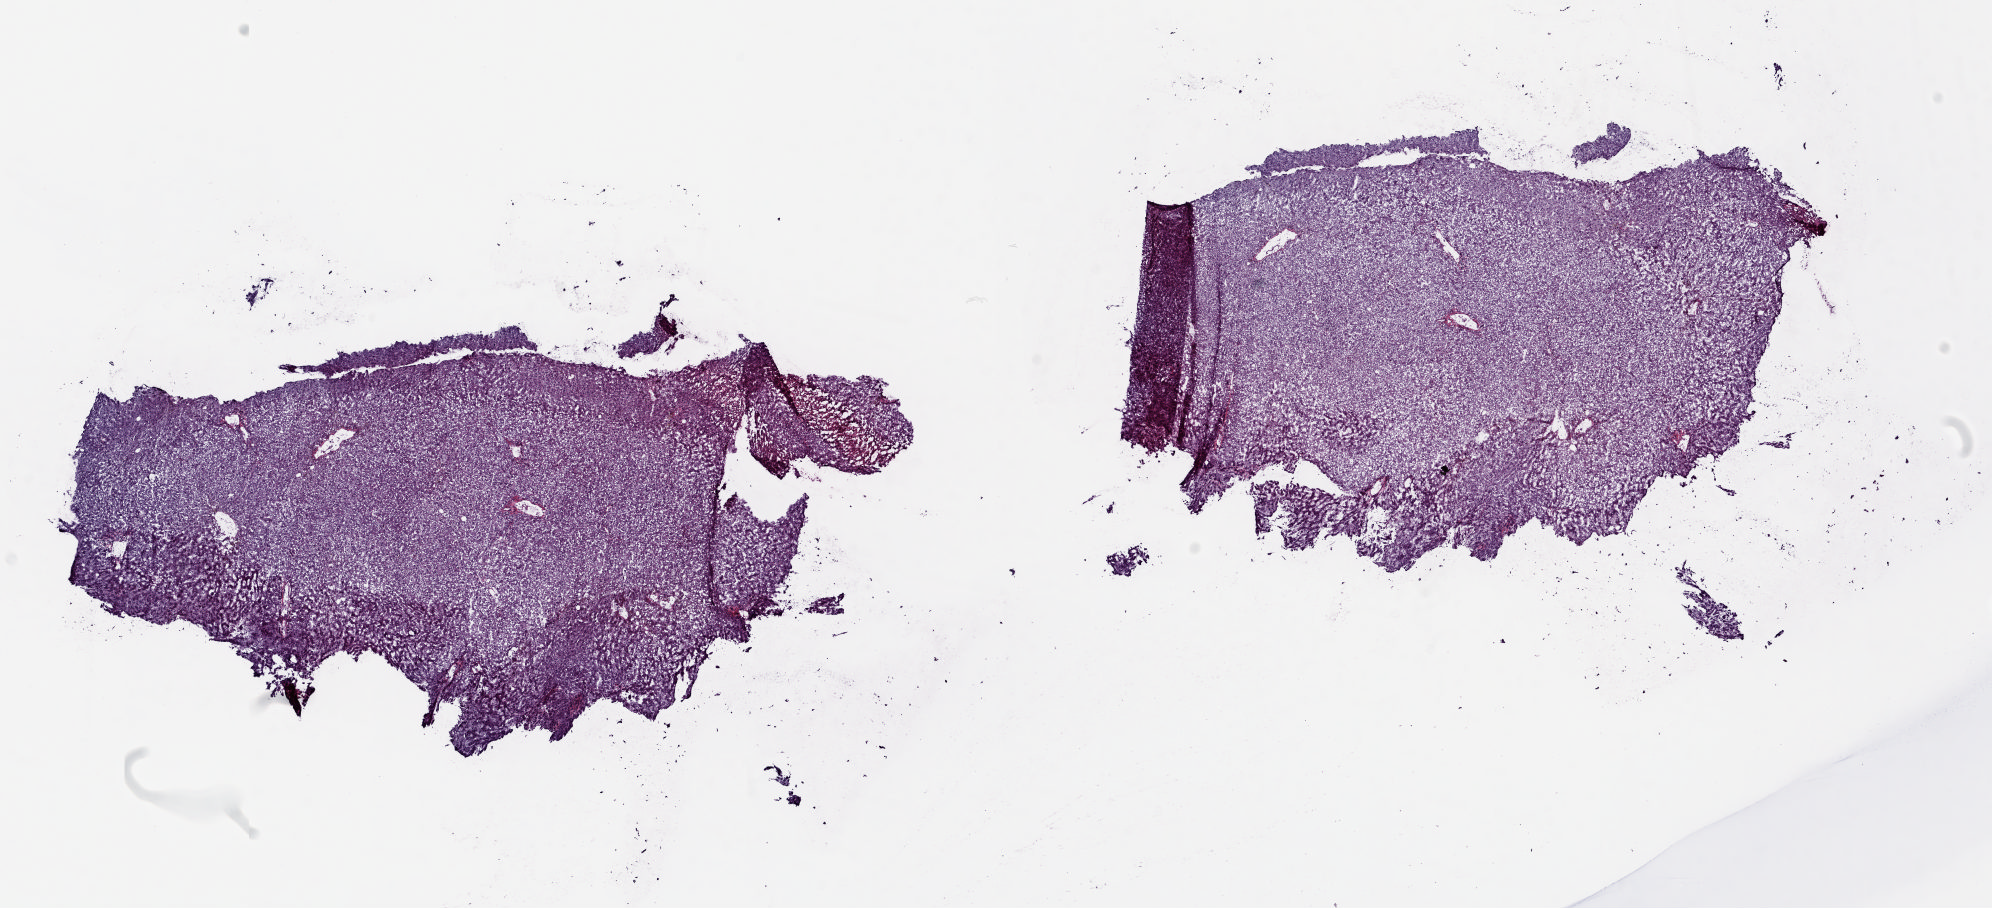
H&E-stained whole-slide image, low-resolution overview of the scanned area, about 15.8 x 7.2 mm. Frozen section. Liver, solid tissue normal (non-tumour tissue) sample. Patient: male, age at initial diagnosis 69 years. Pathologist review of this section (percent, as recorded): tumour cells 0%, tumour nuclei 0%, normal cells 75%, stromal cells 25%, necrosis 0%. Infiltration values recorded for this section: lymphocyte infiltration 5%, monocyte infiltration 2%, neutrophil infiltration 0%.
This section: solid tissue normal (non-tumour) sample from the same patient. Patient diagnosis: Hepatocellular carcinoma, NOS.